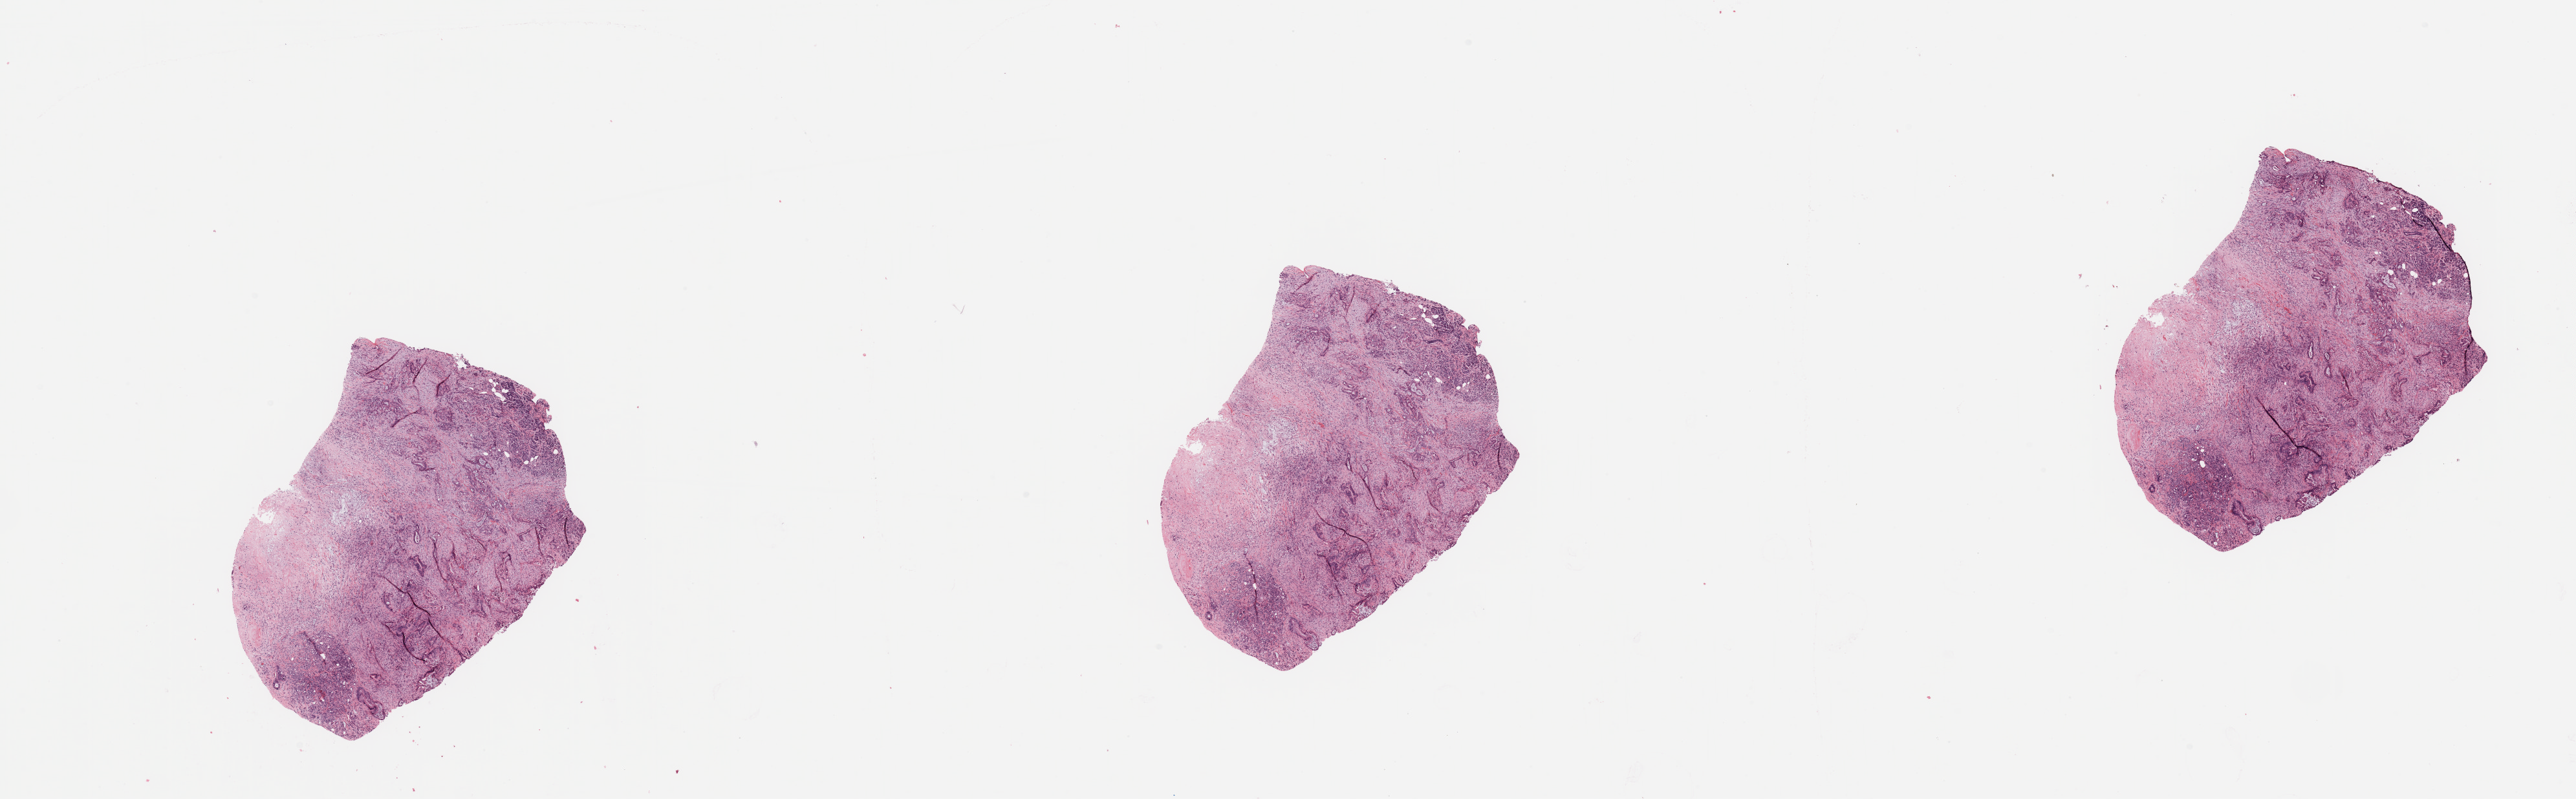
H&E-stained whole-slide image, whole scanned area (about 31.5 x 9.8 mm) shown as a low-resolution overview; pancreas, tumour tissue. 72-year-old male patient. Histologic grade: G1 (well differentiated).
- AJCC pathologic stage: IIB
- primary tumour site (as recorded): head
- histologic diagnosis: Infiltrating duct carcinoma, NOS